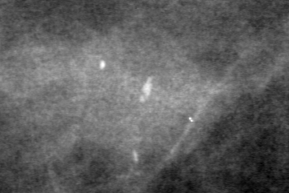
Cropped region of a digitized screen-film mammogram centred on a radiologist-marked abnormality, right breast, CC view, BI-RADS breast density category 1 (scale 1–4).
- Calcifications, morphology pleomorphic, distribution clustered; BI-RADS assessment category 4; subtlety rating 3 on a 1 (subtle) to 5 (obvious) scale; pathology (as recorded): malignant.